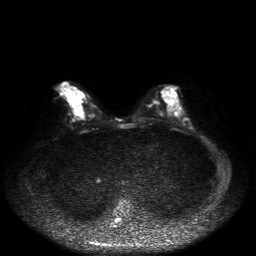
Breast MRI, one axial slice; diffusion-weighted series; image 2 of 4 stored at this slice position (different b-values; order by instance number); 1.5 T; 4 mm slice thickness; 256 × 256 image matrix, field of view 360 × 360 mm. Female patient.
Annotated regions visible in this slice (outlined manually by an expert reader):
- tumour on diffusion-weighted imaging: bounding box (x1, y1, x2, y2) in pixels: (76, 108, 78, 110)